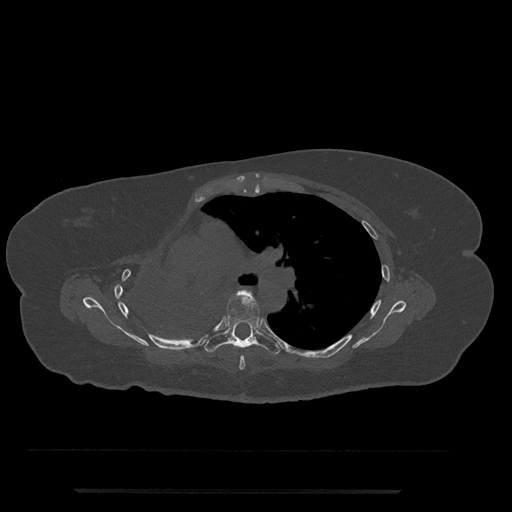
CT including the spine, one axial slice; position 507 of 797 along the scan axis; 120 kVp; bone window (W 1800 / L 400 HU); 512 × 512 image matrix, field of view 440 × 440 mm. Patient: female, 51 years. From the clinical record (not read from this slice): primary cancer: neuro; vertebrae with lytic lesions (as recorded): T8.
Structures marked on this image (semi-automatic segmentation, software-assisted and operator-edited):
- T5 vertebra: bounding box [x1, y1, x2, y2] px = [239, 319, 264, 370]
- T6 vertebra: [205, 291, 280, 355]